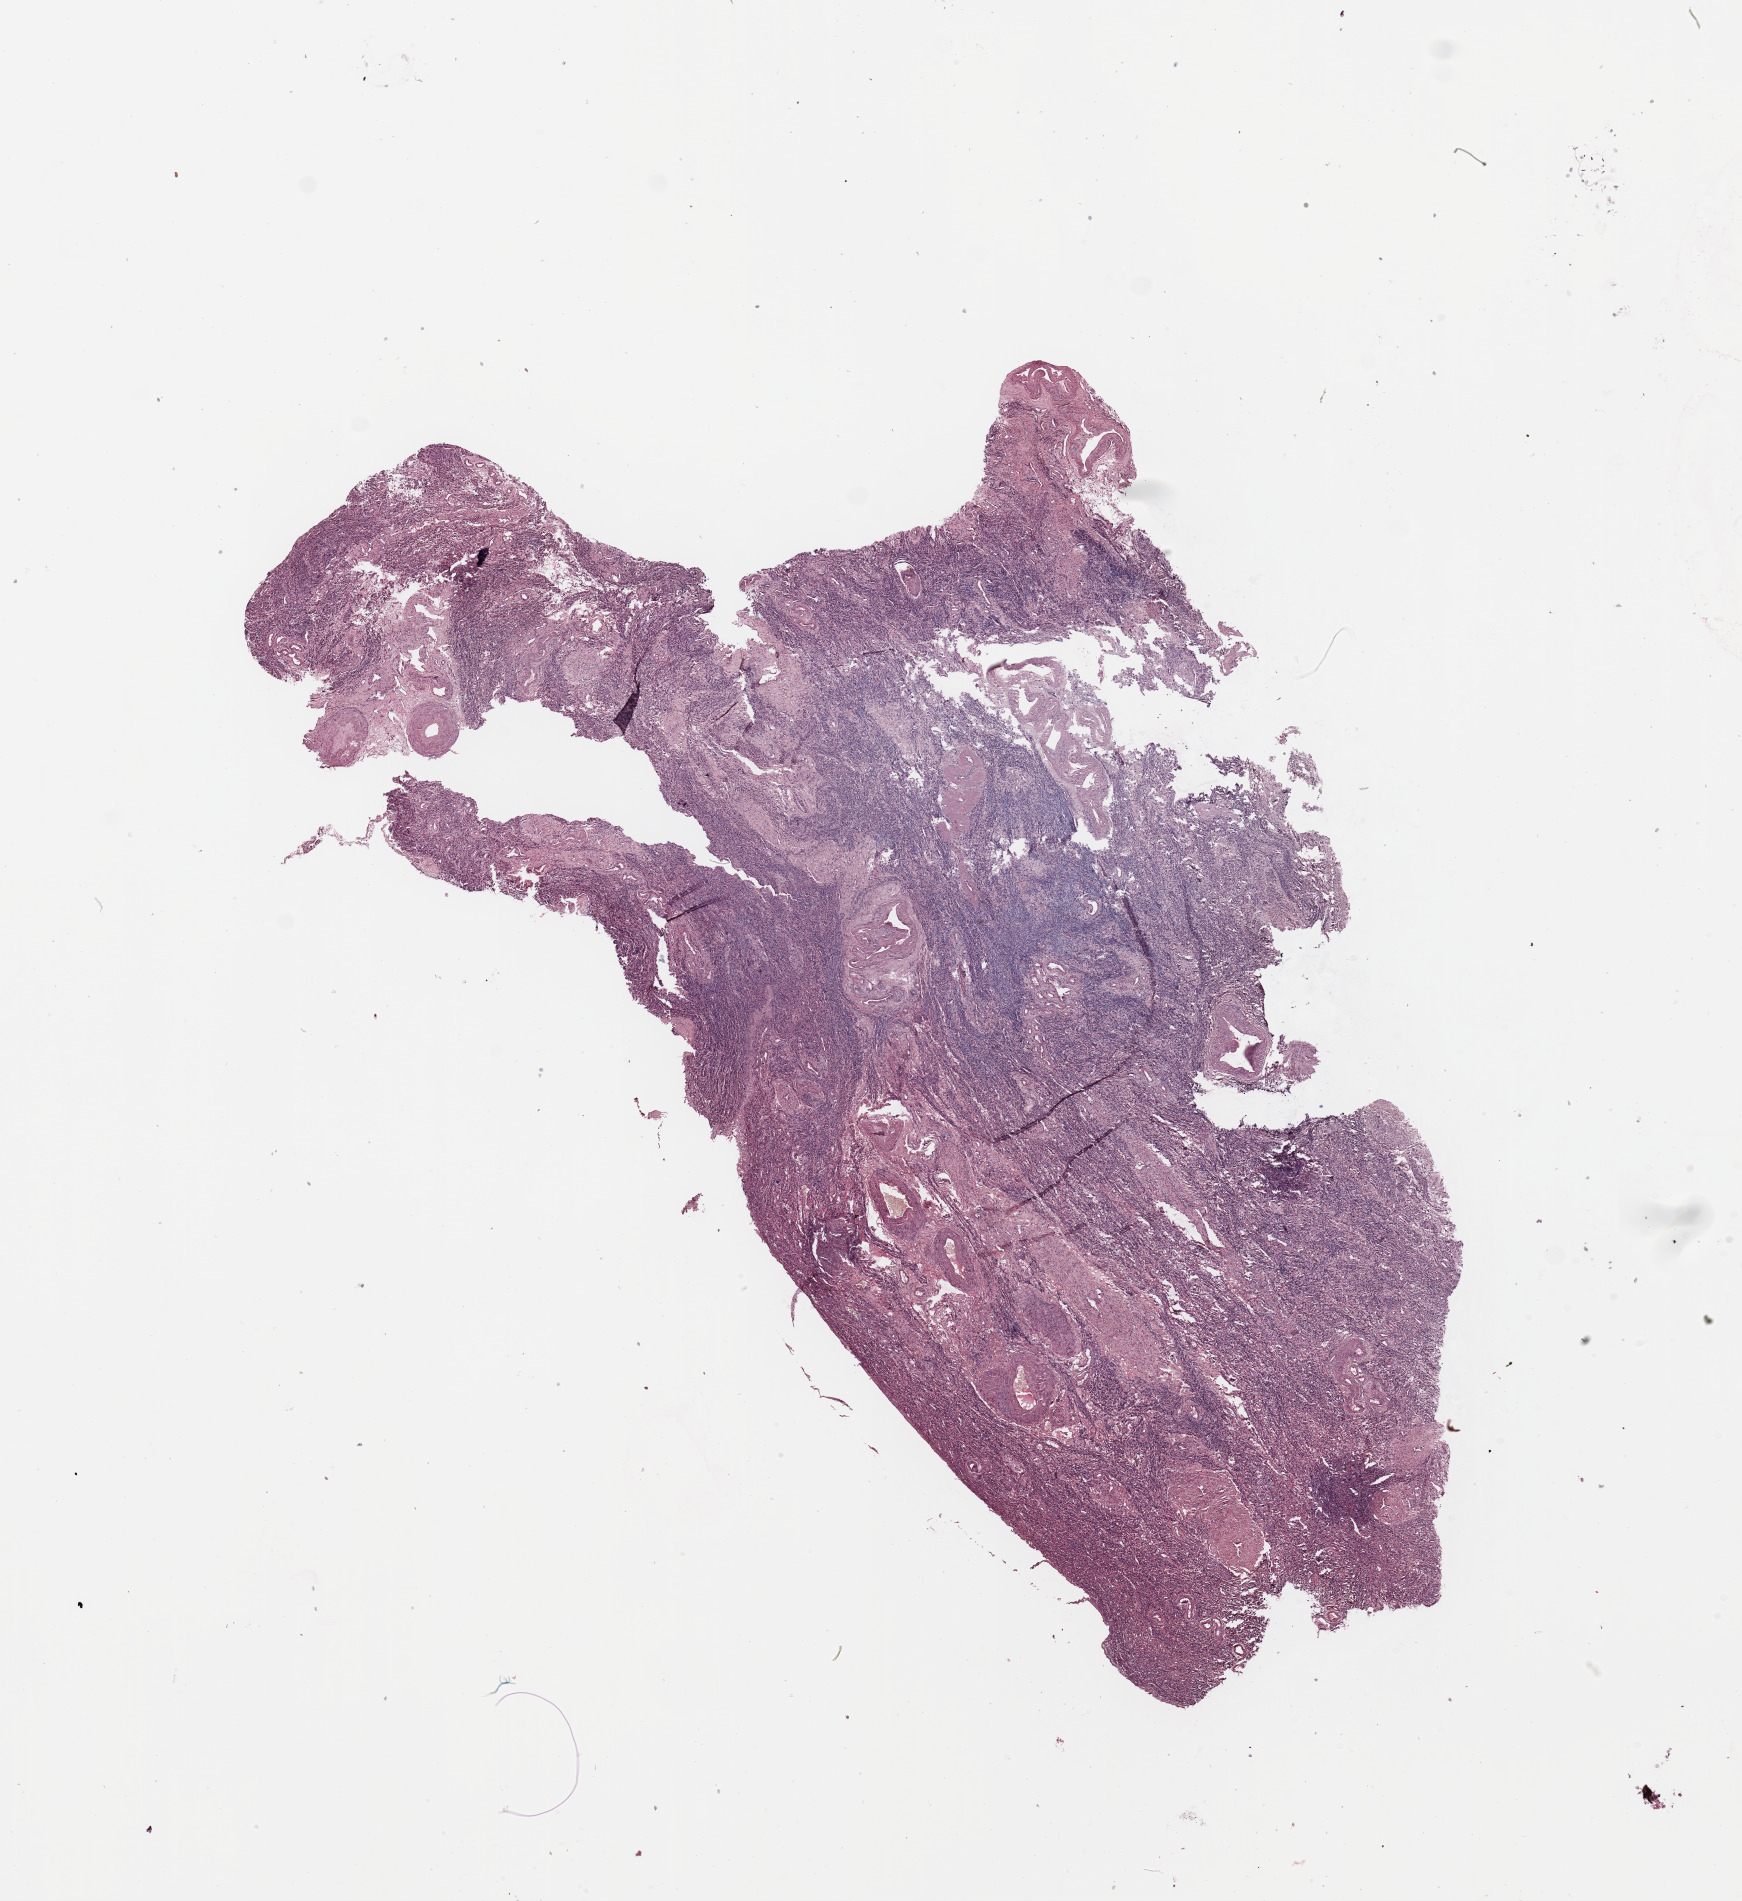
Digitized H&E-stained tissue section (whole slide), shown as a low-resolution overview of the whole scanned area (about 13.8 x 15.0 mm), normal (non-tumour) tissue sample, uterus. Female, 74 y/o.
• this section: normal (non-tumour) tissue from the same patient
• patient diagnosis: Endometrioid adenocarcinoma, NOS